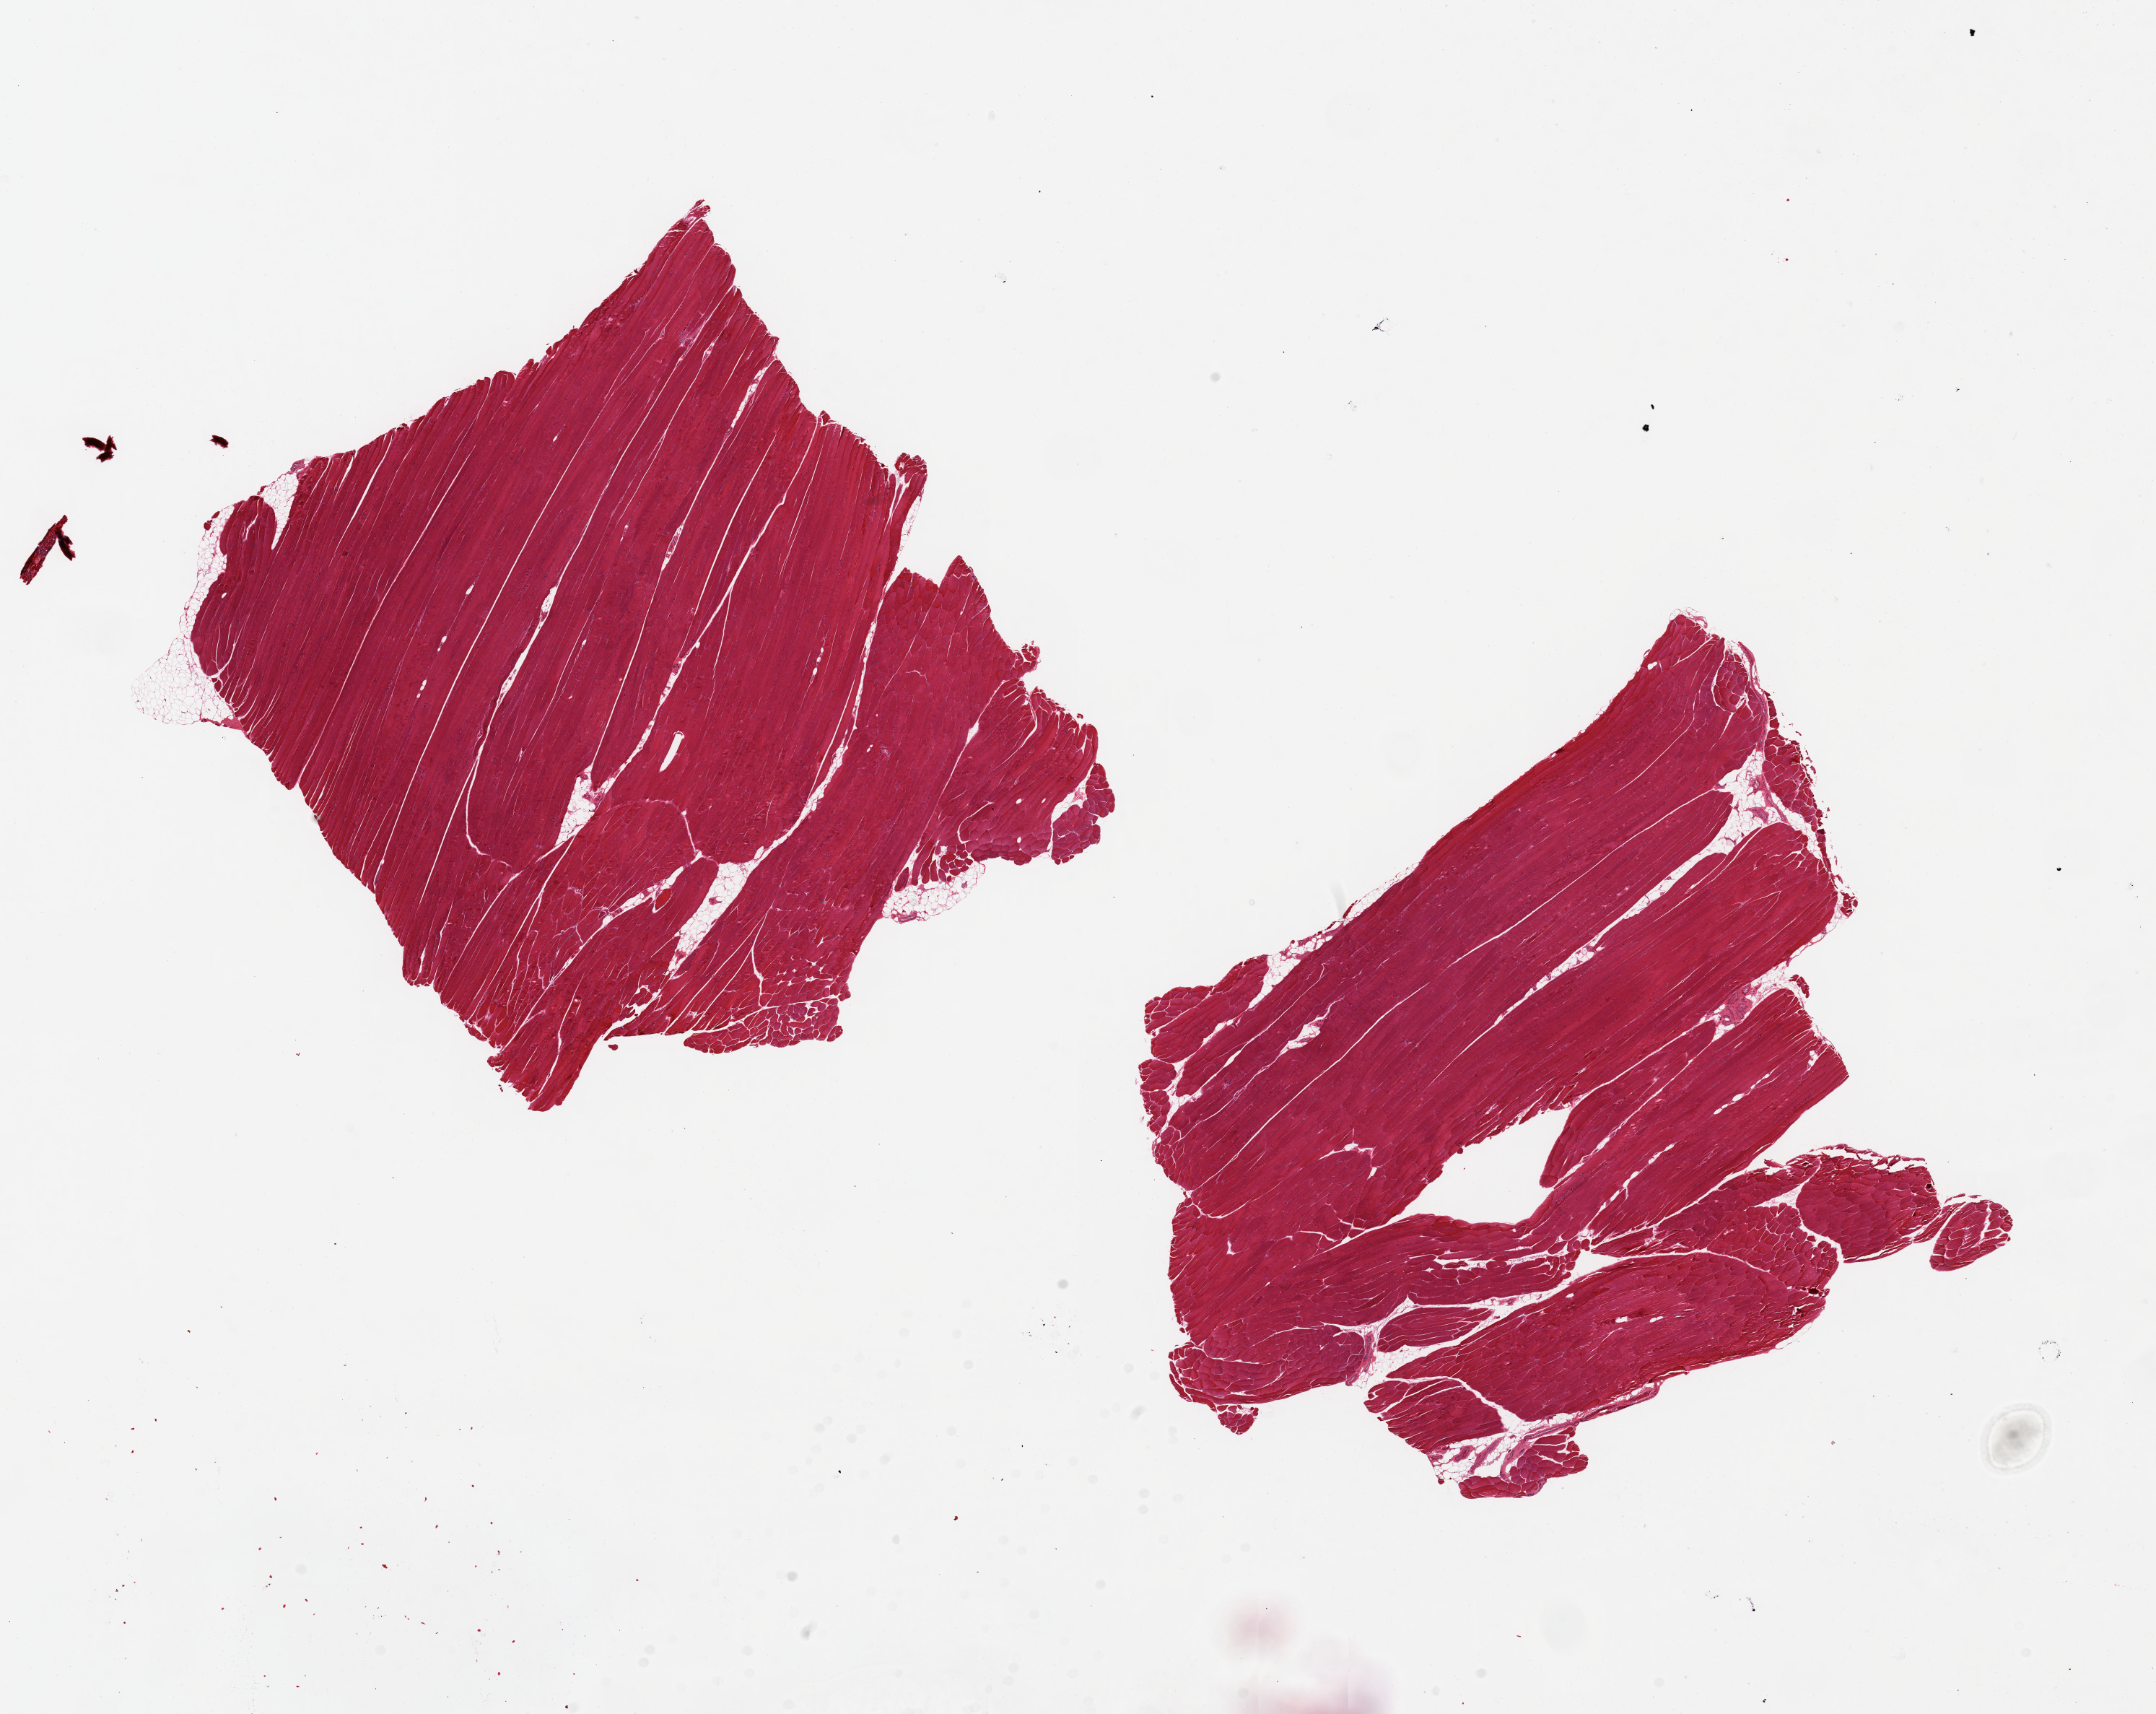
Whole-slide image, H&E stain, whole scanned area (about 23.6 x 18.8 mm) shown as a low-resolution overview. PAXgene-fixed, paraffin-embedded tissue. Sampled site (target tissue): skeletal muscle. Tissue donor sample. Donor sex: male.
Reviewer comment on this tissue sample: 2 pieces, only trace interstitial fat.